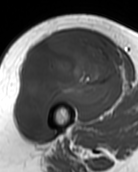
MRI of an extremity soft-tissue mass, one axial slice; position 60 of 99 along the scan axis; MR volume resampled by the dataset authors to the PET/CT grid (not the native acquisition matrix); 3.27 mm slice thickness; 138 × 172 image matrix. Female patient. From the clinical record (not read from this slice): histological type: pleiomorphic undifferentiated sarcoma; grade: high; site of the primary tumour: right quadricep.
Annotated regions visible in this slice (expert contour drawn on MRI and transferred to this co-registered scan by the dataset authors):
- gross tumour volume including surrounding oedema: box from (x=16, y=34) to (x=120, y=133) px
- gross tumour volume (mass): (x=16, y=34)–(x=120, y=133)